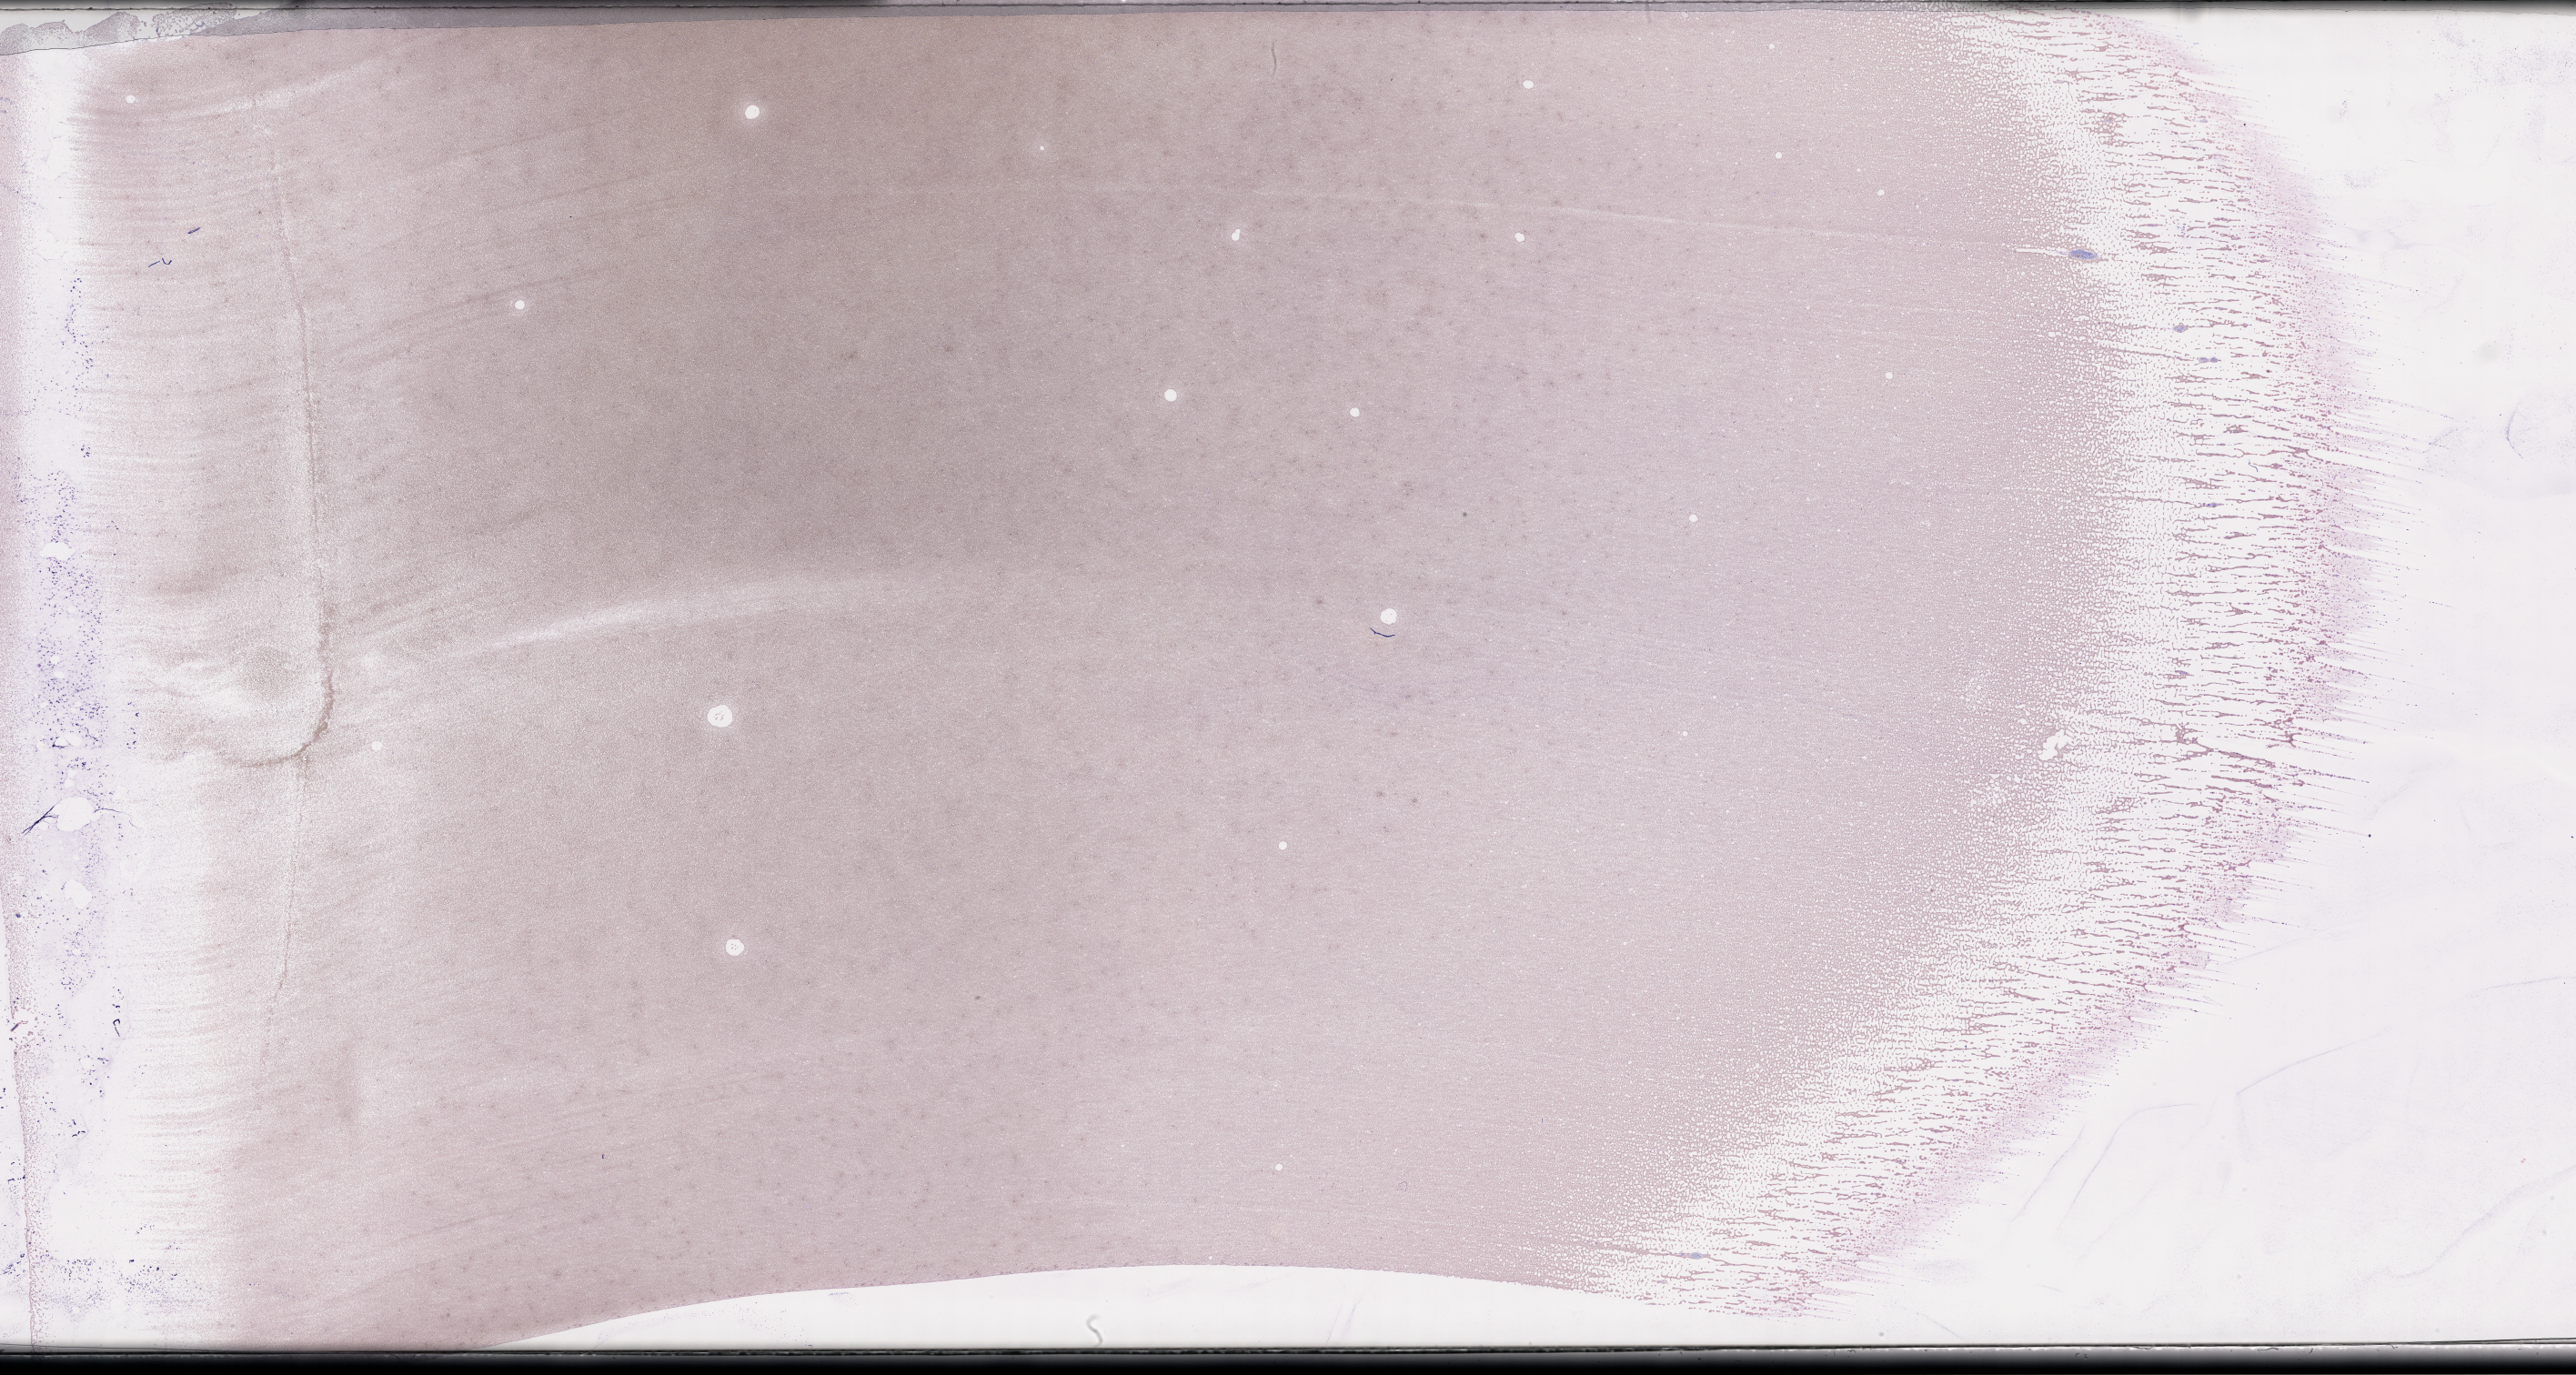
Whole-slide image of a whole blood smear, Wright-Giemsa stain, a low-resolution overview of the entire scanned area, about 45.7 x 24.4 mm; EDTA-anticoagulated smear; specimen time point: collected on treatment. Male patient.
Patient diagnosis: Plasma Cell Myeloma.